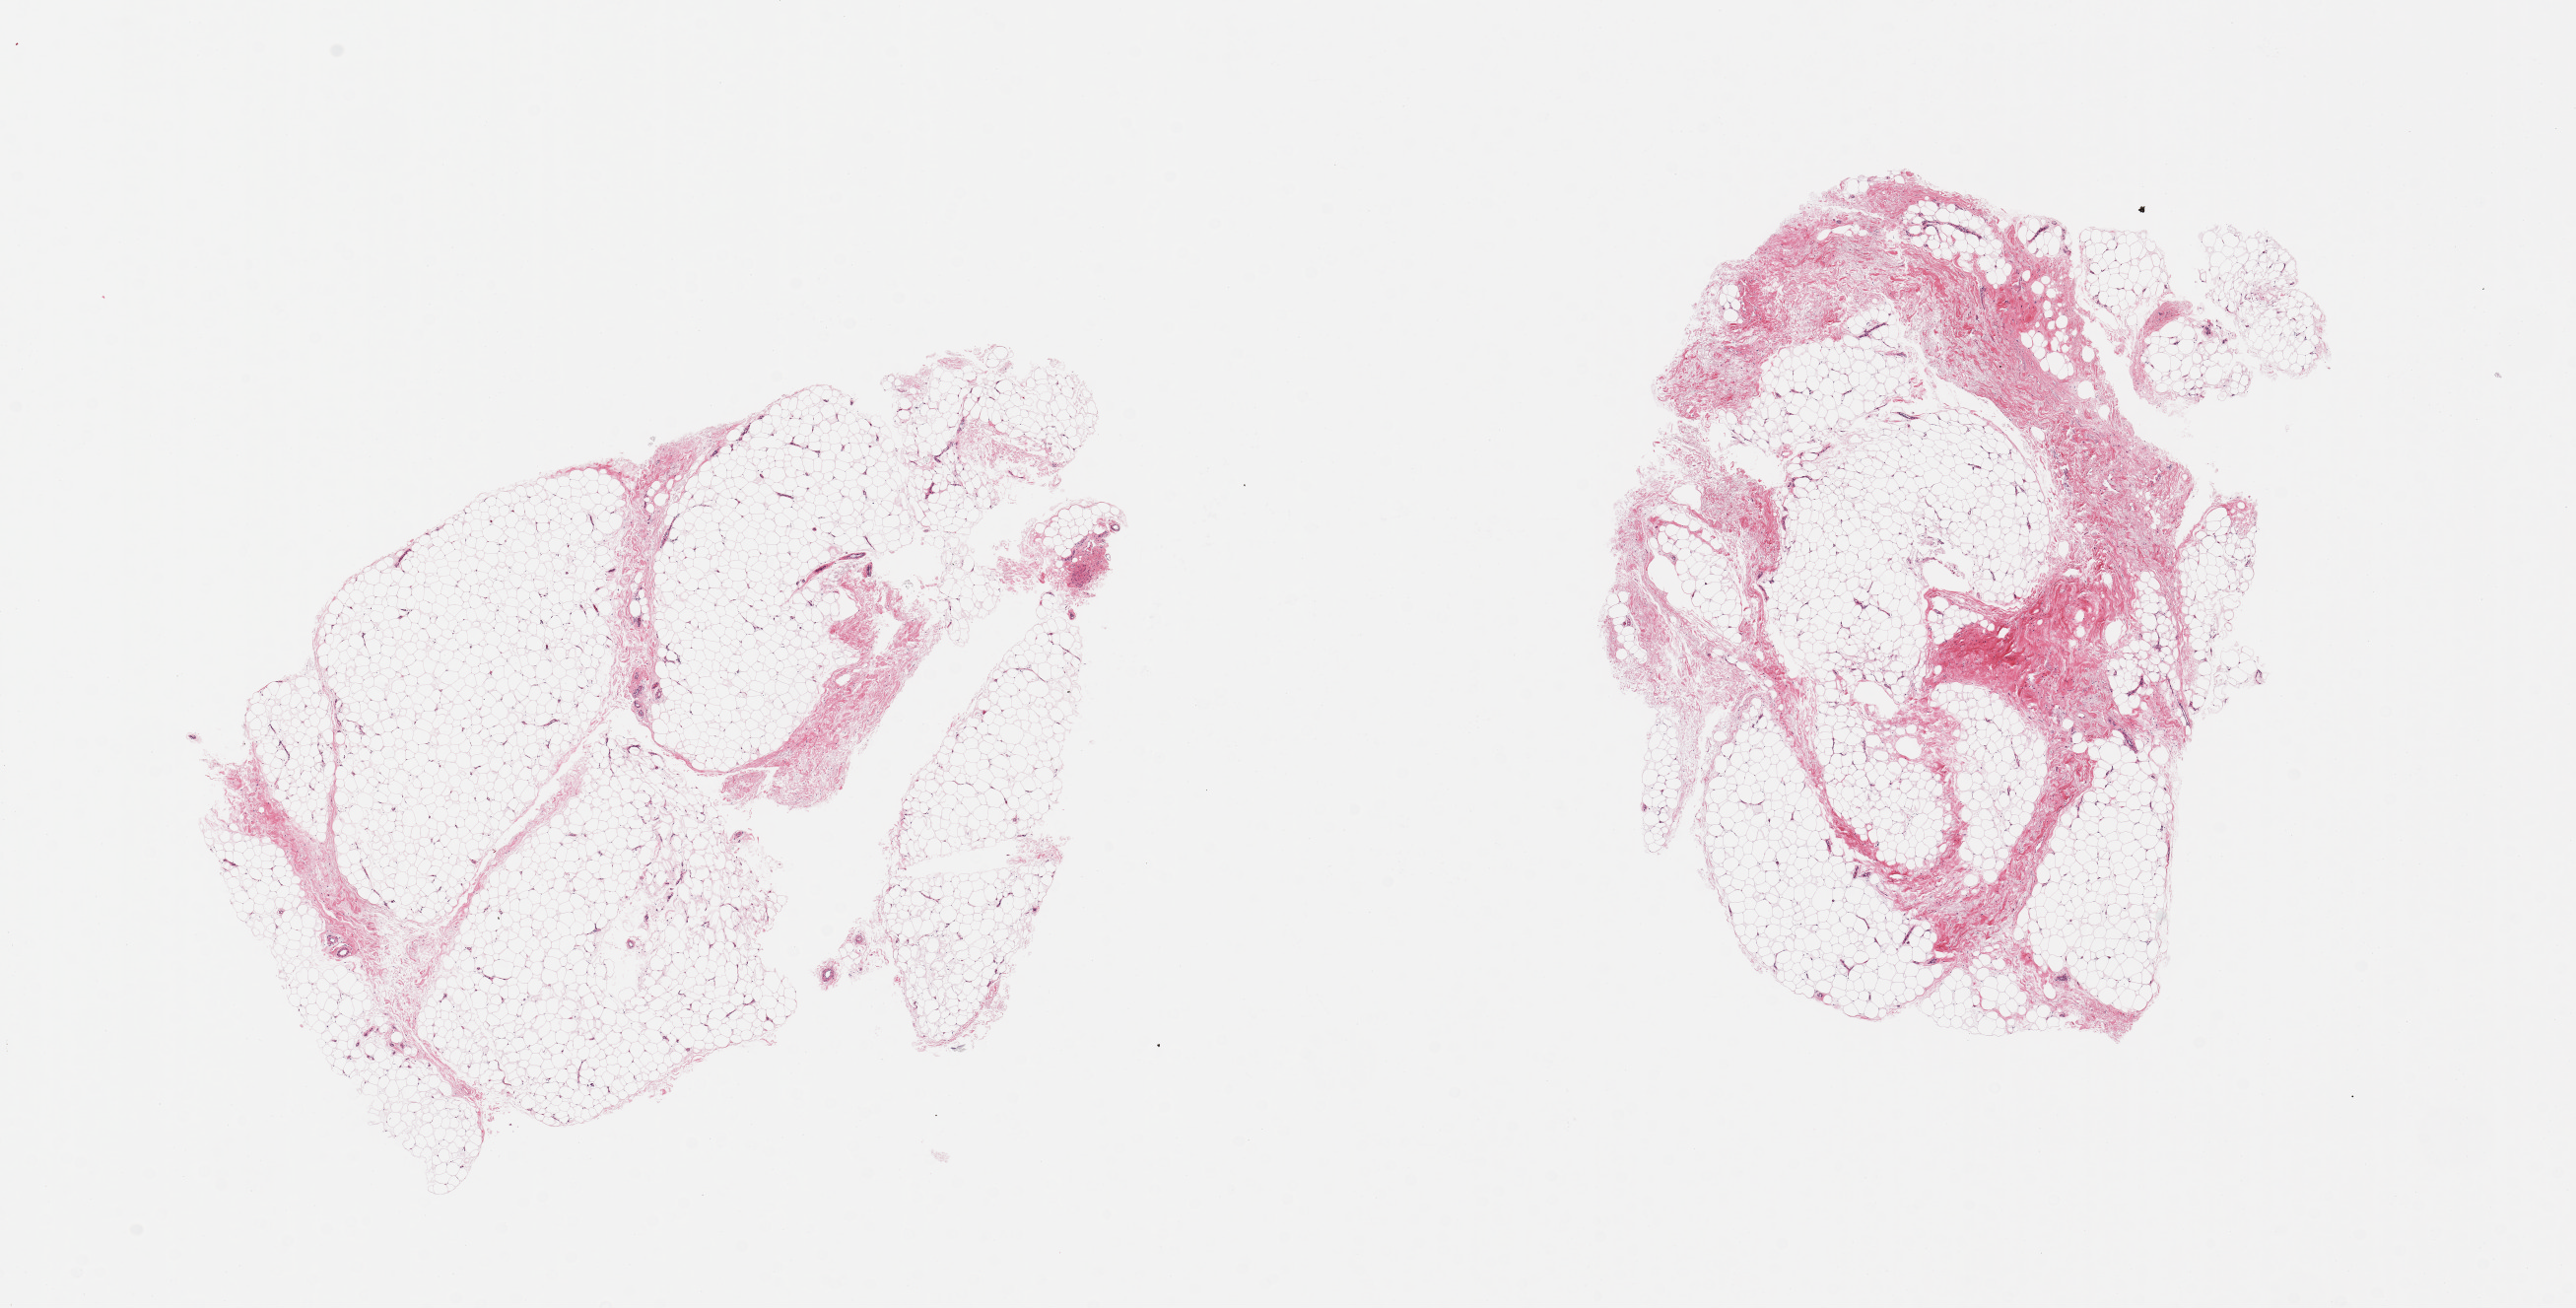
Haematoxylin and eosin whole-slide image, a low-resolution overview of the entire scanned area, about 20.7 x 10.5 mm (acquisition: 20x scan); PAXgene-fixed, paraffin-embedded tissue; target tissue: adipose tissue; tissue donor sample. Donor: male.
Review note (as recorded): 2 pieces, fascia elements are ~40%.